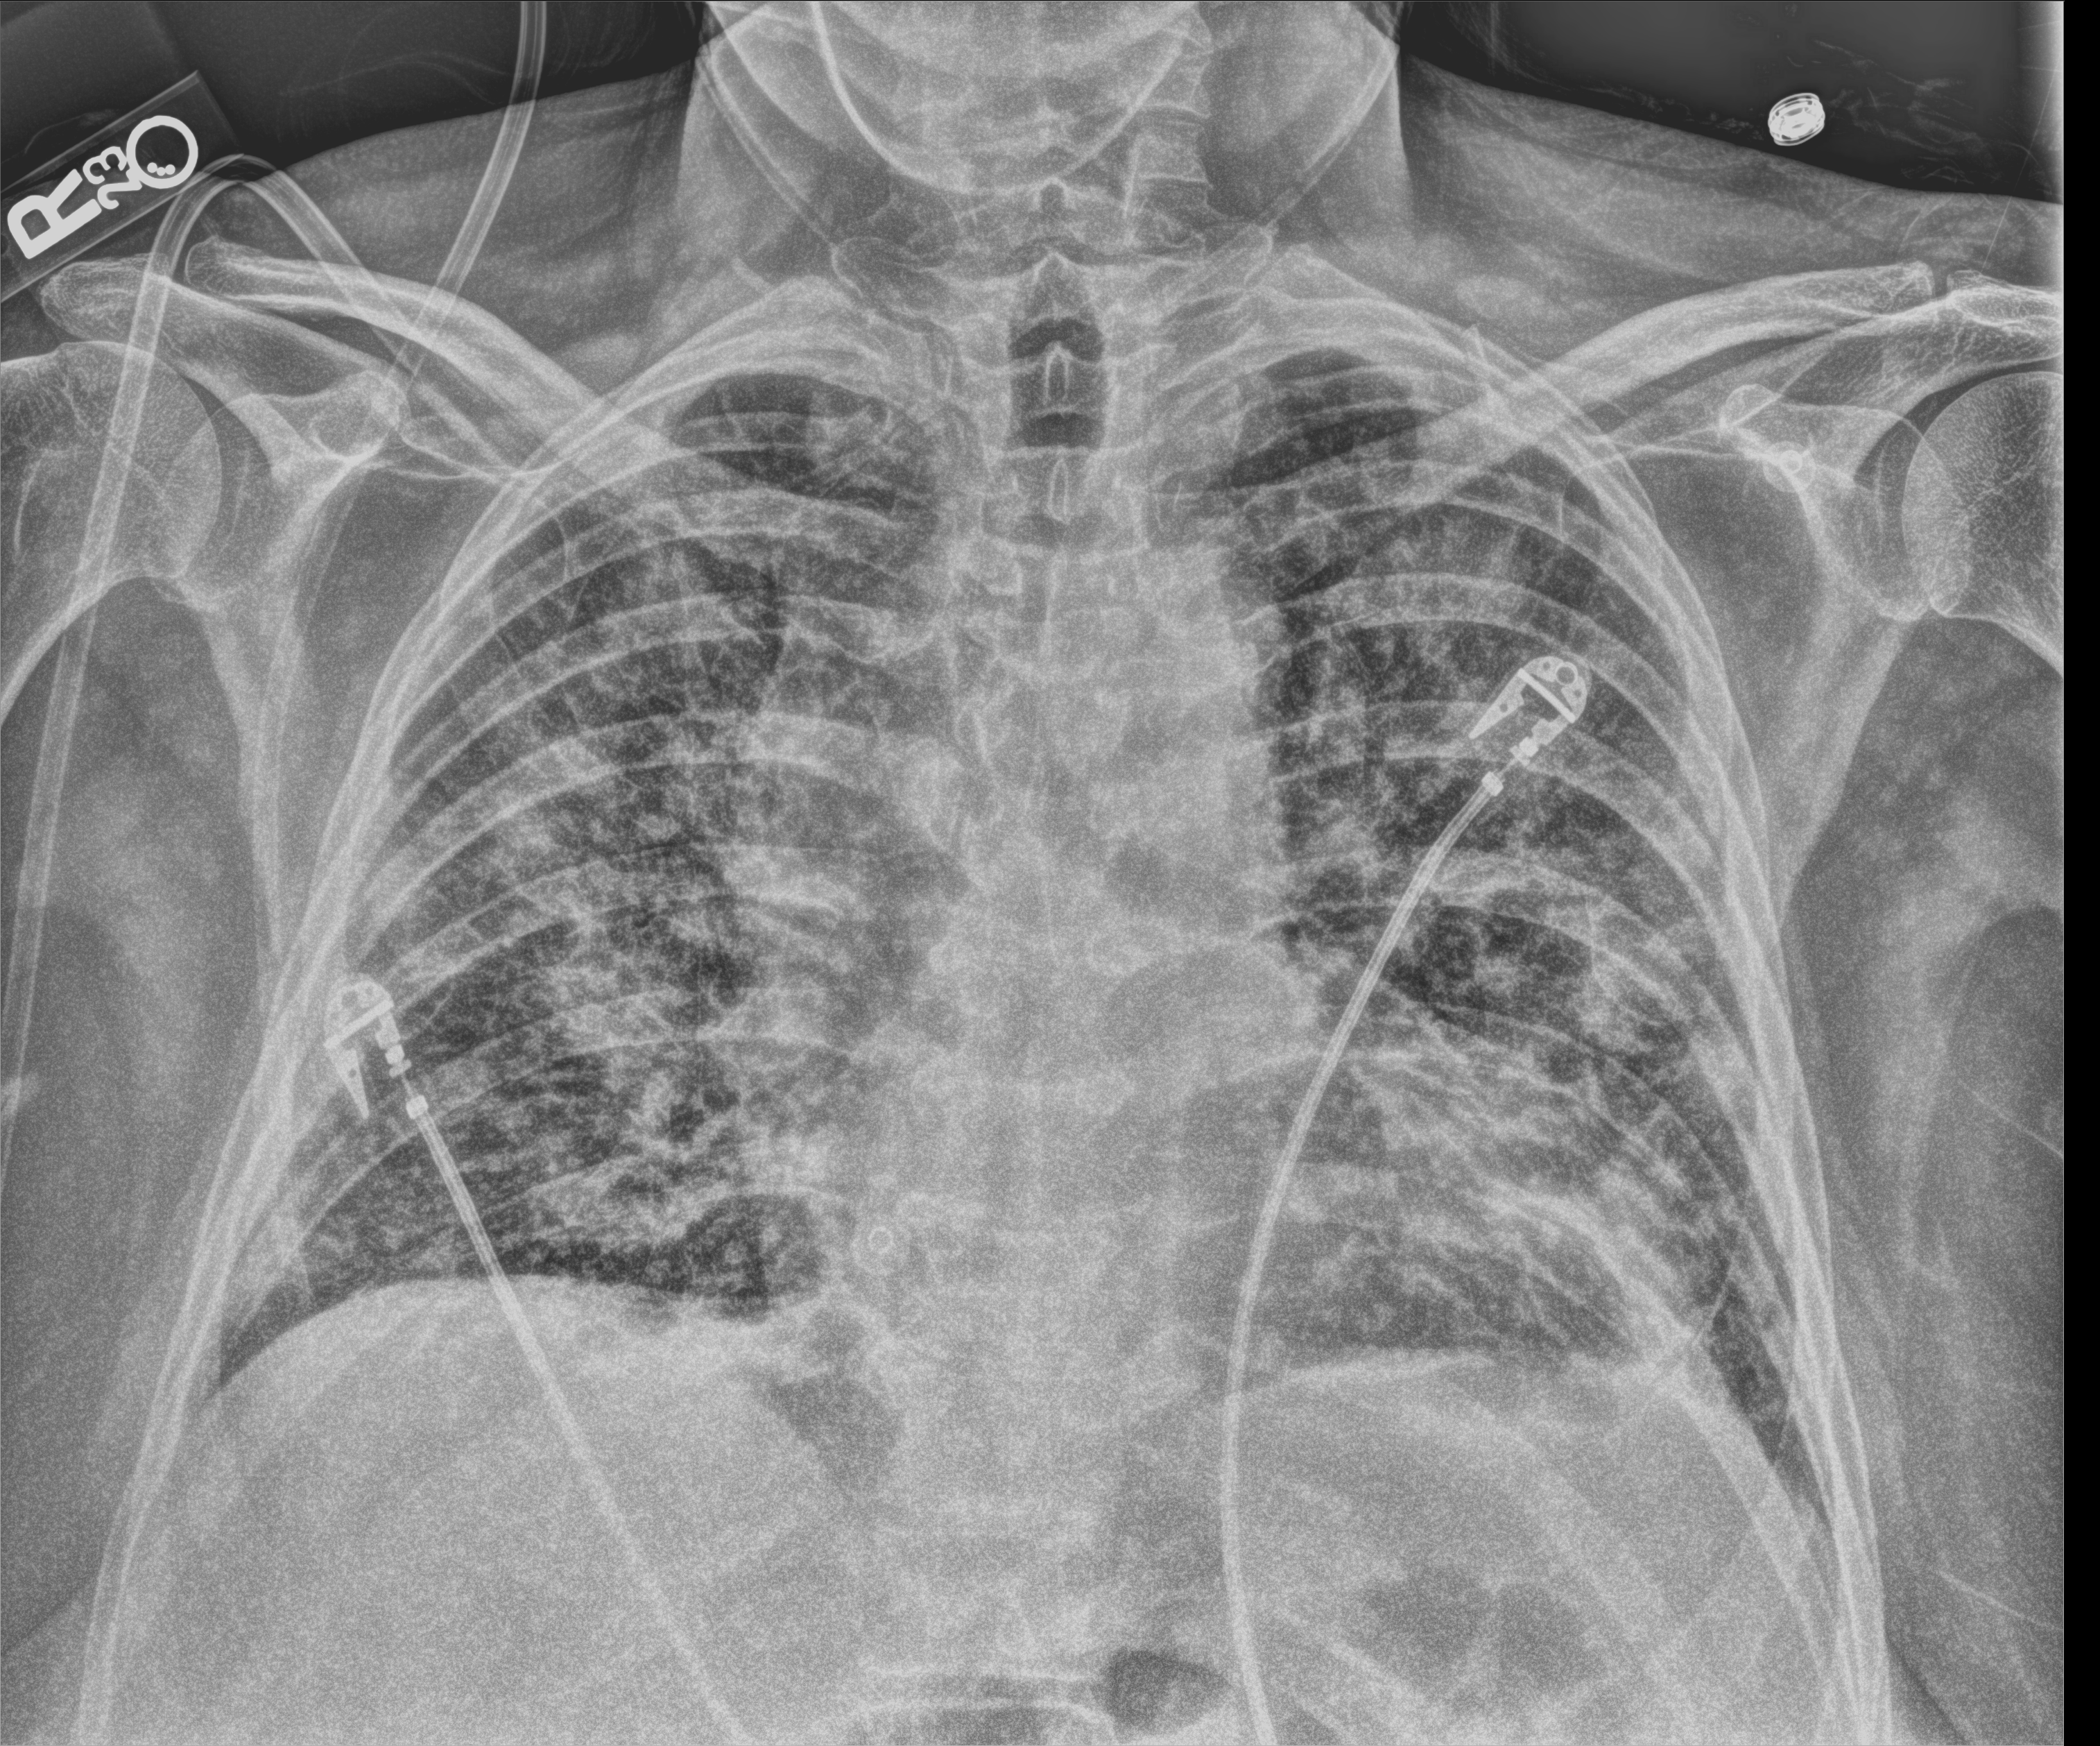
Chest X-ray (portable); anteroposterior (AP) projection. Patient hospitalised with COVID-19; female, aged 60–74 years.
Admission-level facts for this patient (not findings on this image; timing relative to this image not recorded): length of hospital stay: 18 days; COPD (admission record): no.